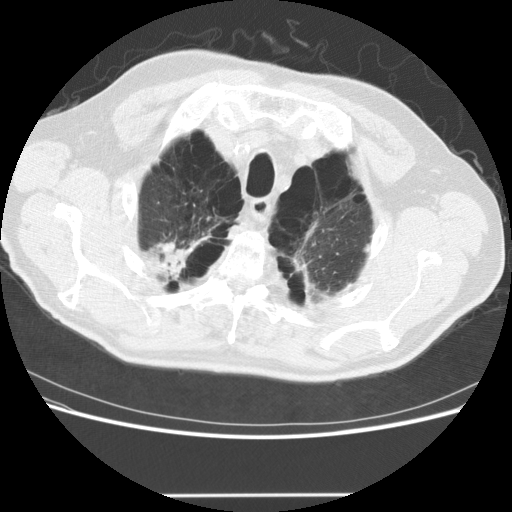
Low-dose screening chest CT, one axial slice; reconstruction kernel STANDARD; 120 kVp; lung window (W 1500 / L -600 HU); 2.5 mm slice thickness; 512 × 512 image matrix, field of view 360 × 360 mm.
Structures marked on this image (expert manual segmentation):
- lesion 1 (tumor, upper lobe of right lung): bounding box [x1, y1, x2, y2] px = [157, 241, 188, 283]